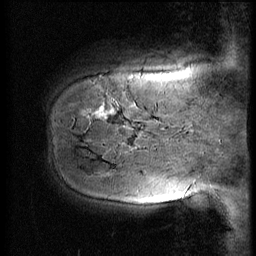
Breast MRI (dynamic contrast-enhanced), one sagittal slice; slice 9 of 56 in the series (ordered by position); 3 images stored at this slice position (order not interpretable as contrast timing); 1.5 T; TE 4.2 ms, TR 9 ms; 2.5 mm slice thickness; 256 × 256 image matrix. Patient: female, 51 years. Case-level facts recorded for this patient, not image findings: setting: breast cancer imaged before/during neoadjuvant chemotherapy; receptor status: HR-positive, HER2-negative.
Structures marked on this image (semi-automatically segmented with operator editing):
- analysis volume of interest (the breast-tissue region the enhancement analysis was run in; not a lesion): bounding box <45,58,167,161> (left, top, right, bottom; pixels)
- tumour enhancement mask (voxels above the 140 % enhancement threshold inside the analysis volume of interest): <93,109,113,119>